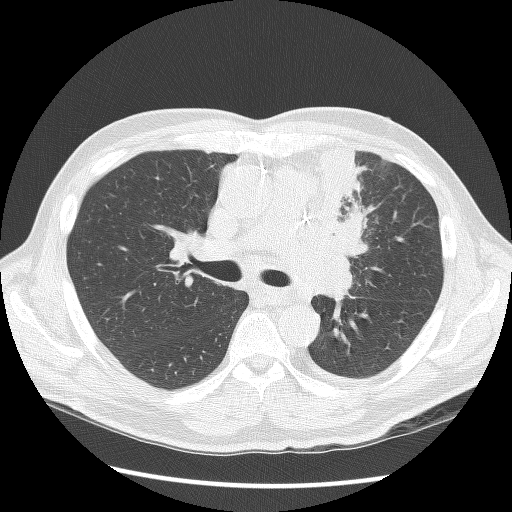
Axial slice from a low-dose chest CT screening exam. Second annual screen. Lung window (W 1500 / L -600 HU). Slice 49 of 136 in the series. Male participant, aged 64 years at enrolment. Former smoker at enrolment.
- Expert-annotated lung lesion, bounding box (x1, y1, x2, y2) in pixels: (301, 149, 381, 284).
- No non-calcified nodule or mass ≥4 mm was recorded by the screening reader at this exam.
- Official screen result: positive, other.